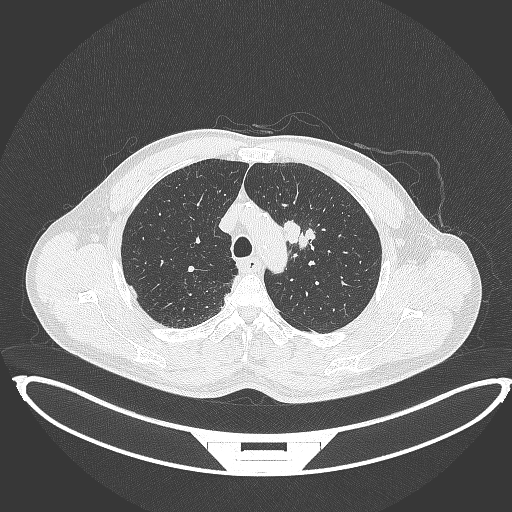
Chest CT, one axial slice; slice 334 of 395 in the series (ordered by position); 120 kVp; lung window (W 1500 / L -600 HU); 1 mm slice thickness; 512 × 512 image matrix, field of view 457 × 457 mm. Male patient, age 60 years. From the clinical record (not read from this slice): clinical TNM (as recorded): T2a N0 M0; histopathological grade: G1-G2.
Structures marked on this image (rectangle marked by the reading radiologist):
- lung tumour (recorded histology: squamous cell carcinoma): bounding box [x1, y1, x2, y2] px = [283, 217, 315, 253]